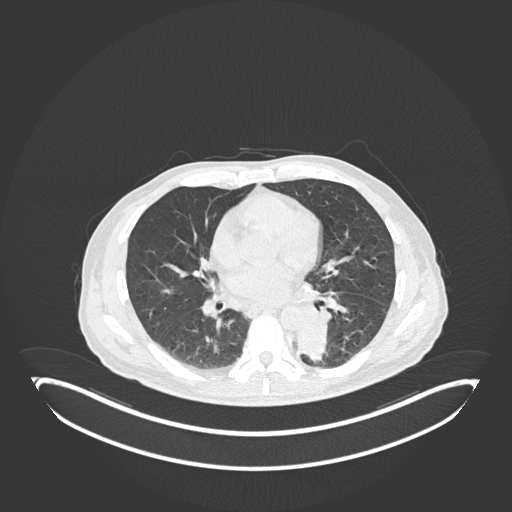
Chest CT, one axial slice. Position 90 of 251 along the scan axis. 120 kVp. Lung window (W 1500 / L -600 HU). 1 mm slice thickness. 512 × 512 image matrix, field of view 500 × 500 mm. Male patient, age 72 years. Case-level facts recorded for this patient, not image findings: clinical TNM (as recorded): T2b N0 M1.
Annotated regions visible in this slice (rectangle marked by the reading radiologist):
- lung tumour (recorded histology: adenocarcinoma): bounding box [x1, y1, x2, y2] px = [290, 317, 326, 361]